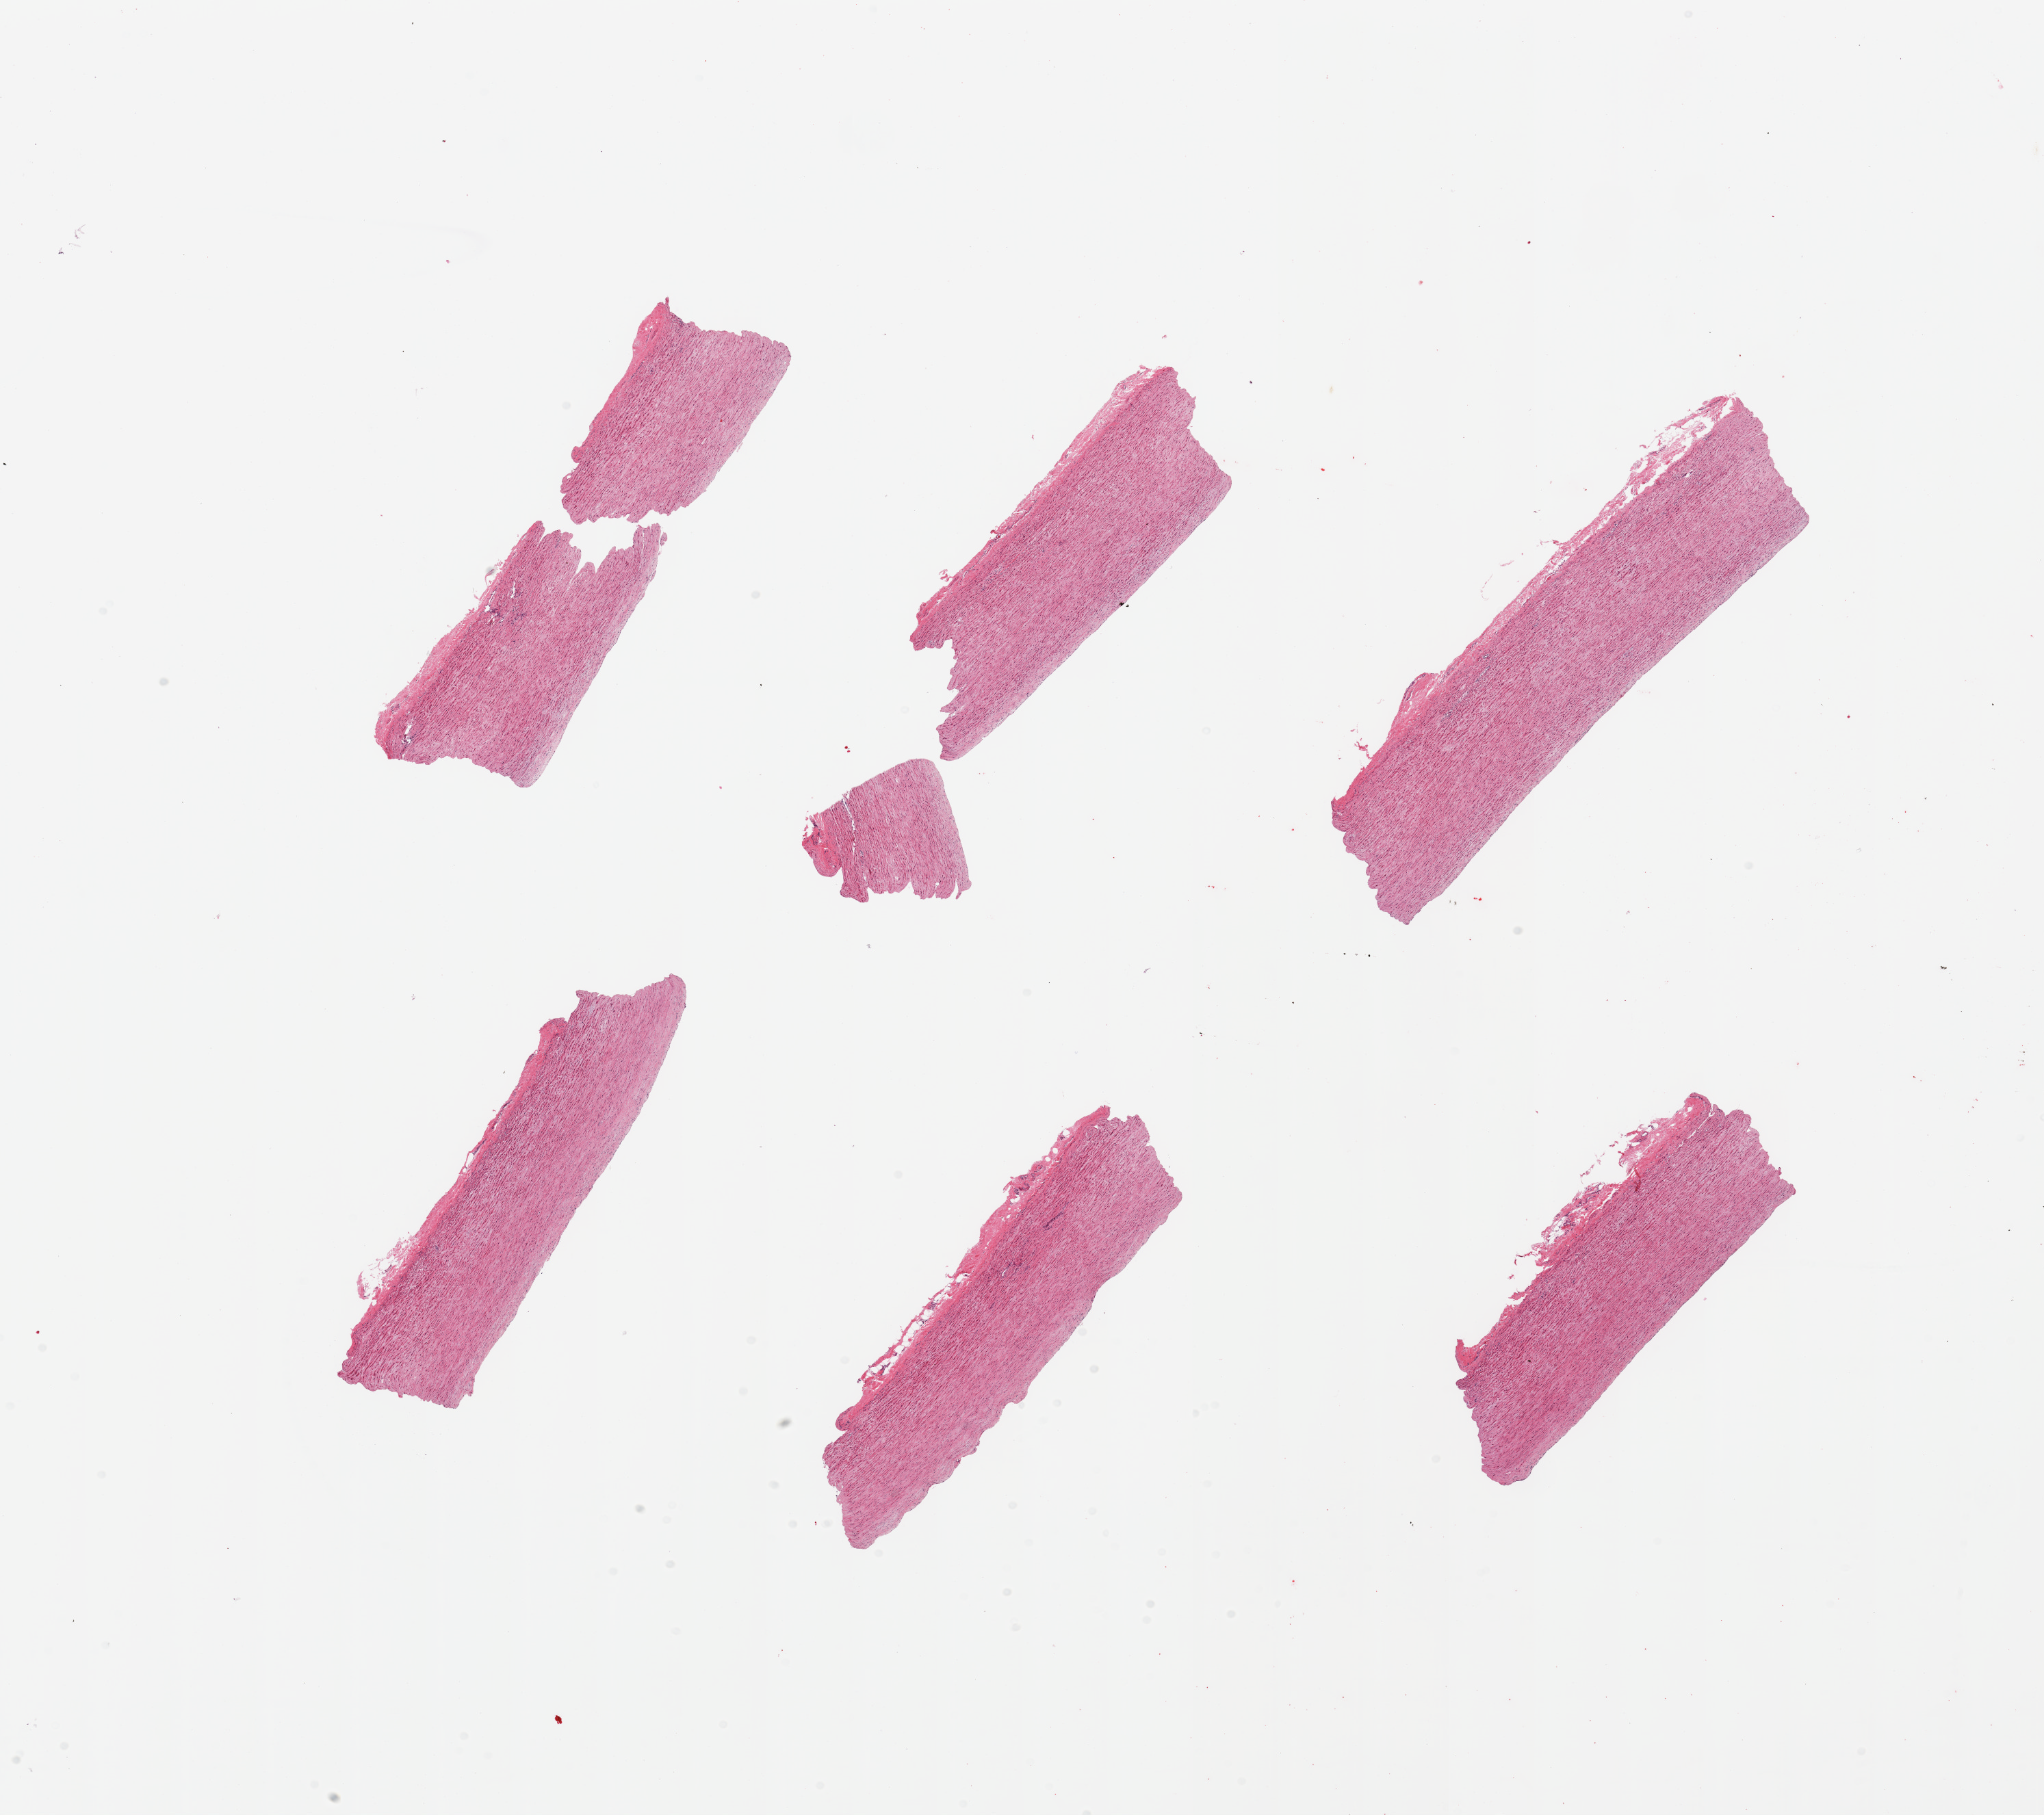
Haematoxylin and eosin whole-slide image, low-resolution overview of the scanned area, about 23.6 x 21.0 mm; PAXgene-fixed paraffin-embedded (PFPE) section; sampled site (target tissue): aorta; donor tissue sample. Male donor.
* pathologist's review note for this sample: 6 pieces, minimal atherosis